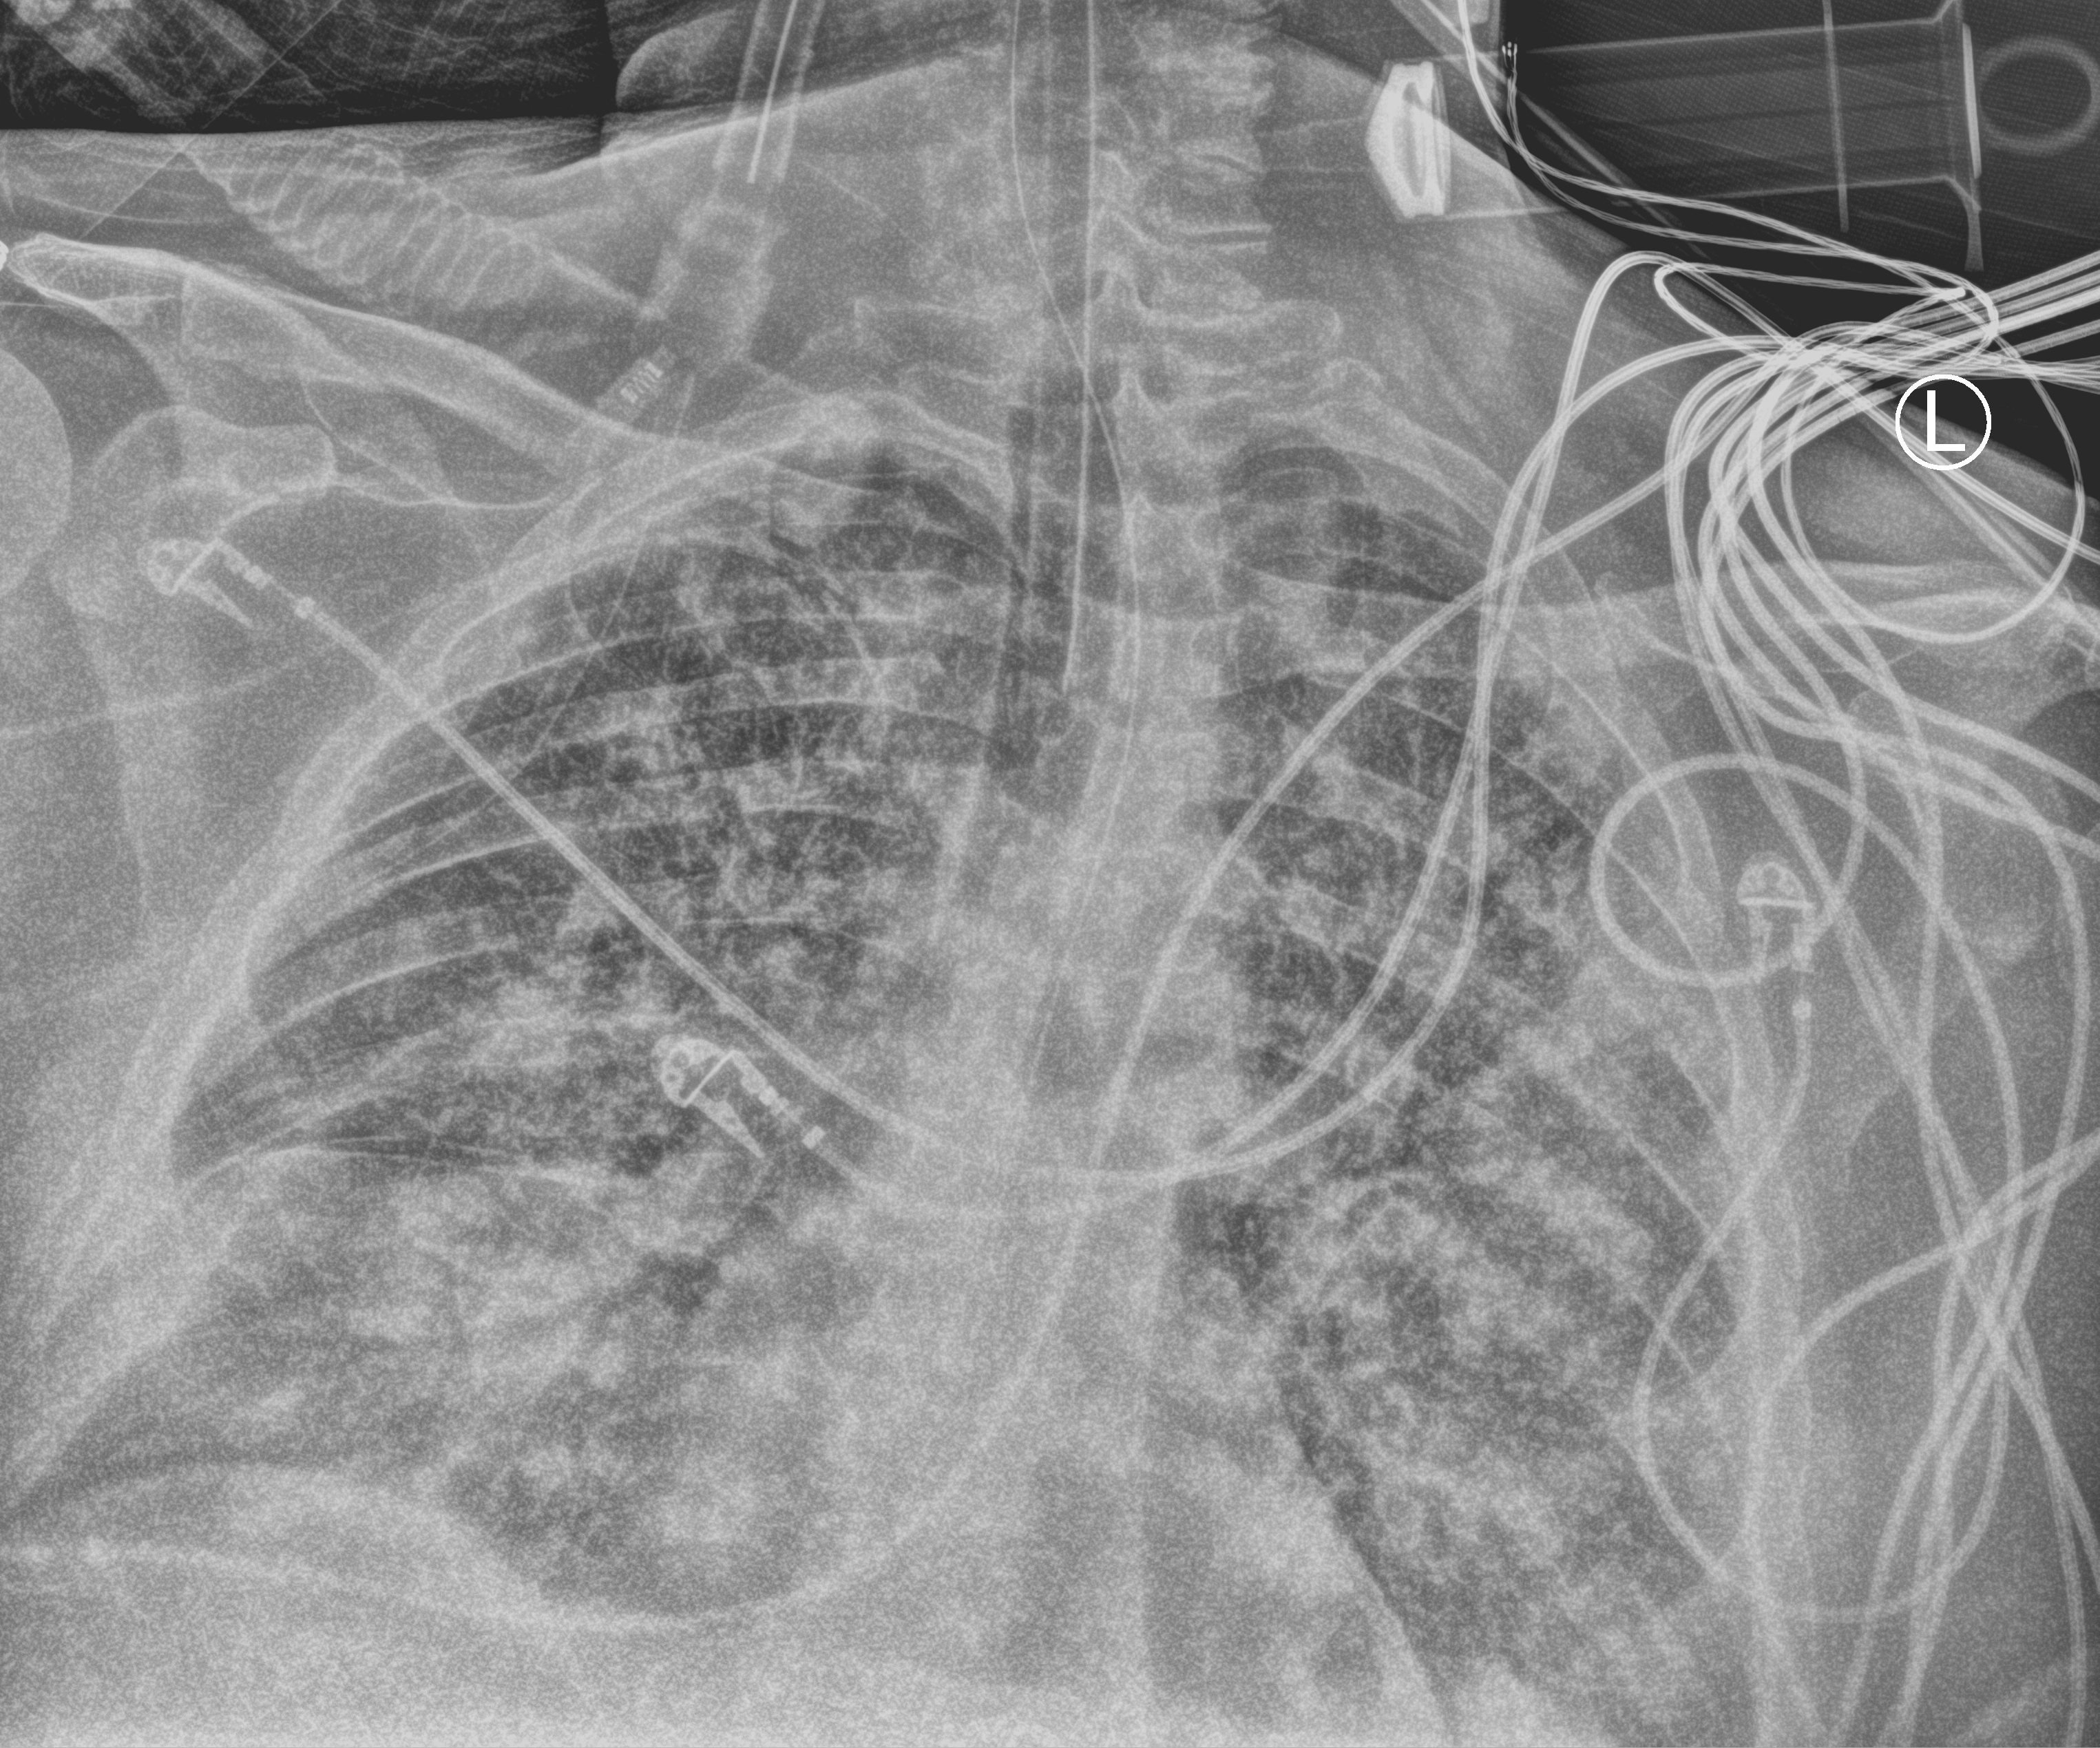
Chest X-ray (portable). Male patient hospitalised with COVID-19, age 60–74 years.
From the hospital-stay record, not from the radiograph (when in the stay this image was taken is not recorded): other chronic lung disease (admission record): yes; admitted to intensive care during this hospital stay: yes; mechanically ventilated during this hospital stay: yes.